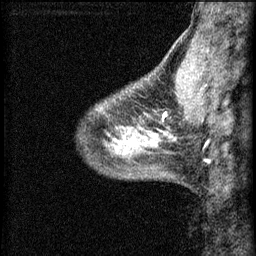
Breast MRI (dynamic contrast-enhanced), one sagittal slice. Position 19 of 60 along the scan axis. 3 images stored at this slice position (order not interpretable as contrast timing). 1.5 T. TE 4.2 ms, TR 8.2 ms. 2.2 mm slice thickness. 256 × 256 image matrix, field of view 180 × 180 mm. Female patient, age 40 years.
Annotated regions visible in this slice (semi-automatic segmentation, software-assisted and operator-edited):
- analysis volume of interest (the breast-tissue region the enhancement analysis was run in; not a lesion): bounding box <108,82,175,139> (left, top, right, bottom; pixels)
- tumour enhancement mask (voxels above the 70 % enhancement threshold inside the analysis volume of interest): <162,114,167,121>